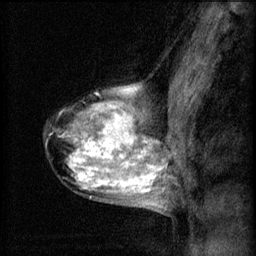
Breast MRI (dynamic contrast-enhanced), one sagittal slice. Slice 42 of 60 in the series (ordered by position). 3 images stored at this slice position (order not interpretable as contrast timing). 1.5 T. TE 4.2 ms, TR 8.2 ms. 256 × 256 image matrix. Patient: female, 40 years.
Annotated regions visible in this slice (semi-automatic segmentation, software-assisted and operator-edited):
- analysis volume of interest (the breast-tissue region the enhancement analysis was run in; not a lesion): bounding box <44,80,167,211> (left, top, right, bottom; pixels)
- tumour enhancement mask (voxels above the 70 % enhancement threshold inside the analysis volume of interest): <62,86,161,205>